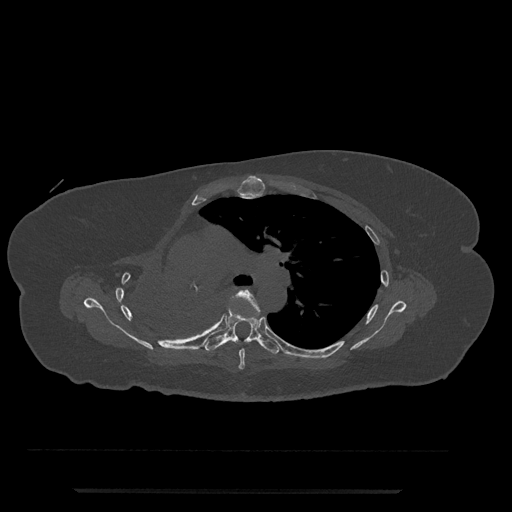
CT including the spine, one axial slice. Position 514 of 797 along the scan axis. Reconstruction kernel Br40s/3. 120 kVp. Bone window (W 1800 / L 400 HU). 0.5 mm slice thickness. 512 × 512 image matrix, field of view 440 × 440 mm. Patient: female, 51 years. From the clinical record (not read from this slice): primary cancer: neuro.
Annotated regions visible in this slice (semi-automatically segmented with operator editing):
- T5 vertebra: box from (x=231, y=289) to (x=265, y=370) px
- T6 vertebra: (x=205, y=309)–(x=280, y=355)